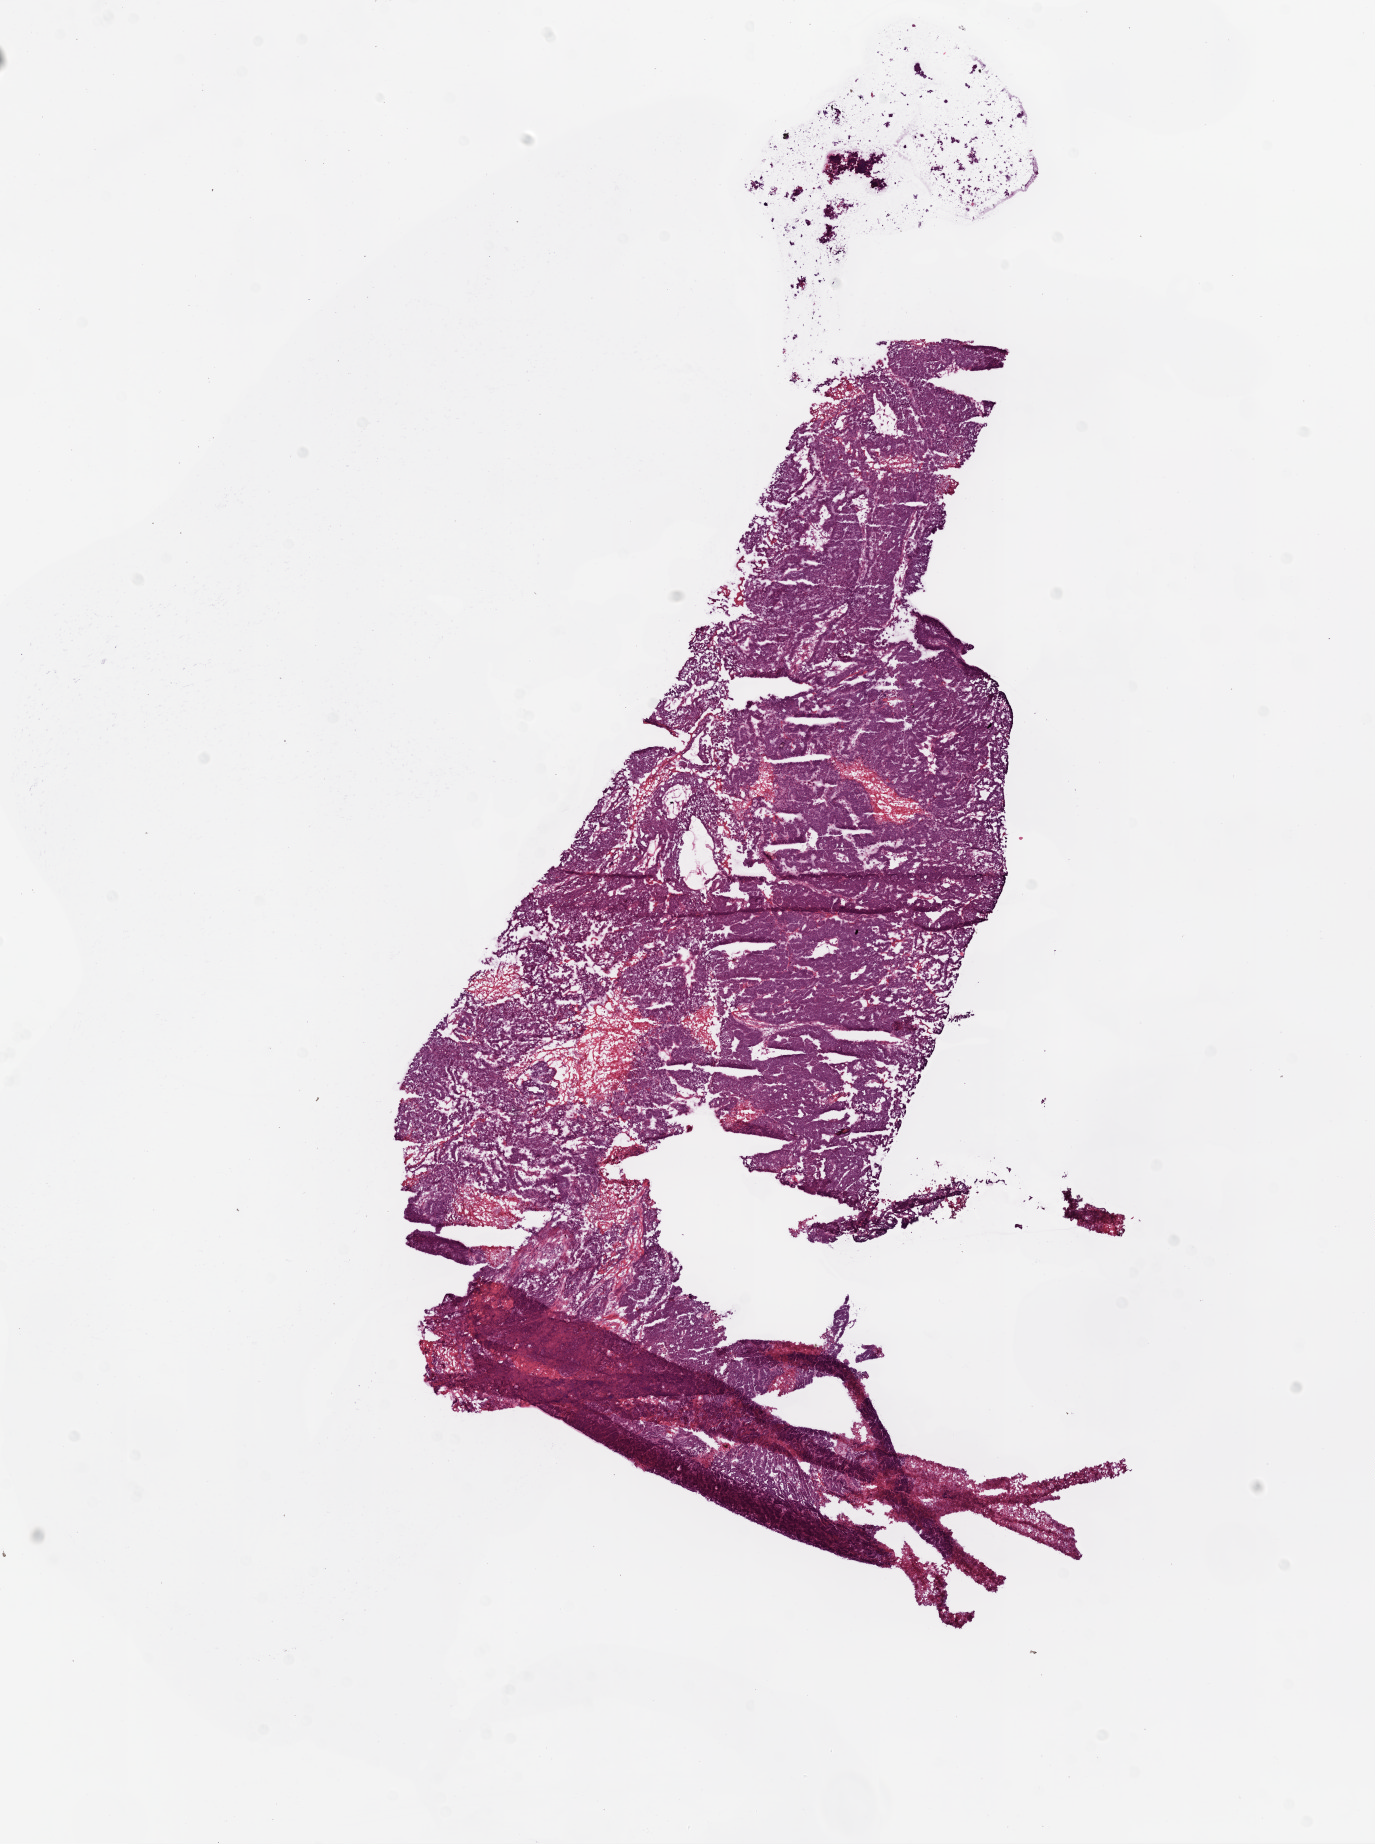
Hematoxylin and eosin (H&E) stained whole-slide image — shown as a low-resolution overview of the whole scanned area (about 11.0 x 14.8 mm, from a 20x scan), frozen section, sample: primary tumour, ovary. Female patient; age at initial diagnosis 42 years. Histologic grade: G3 (poorly differentiated). Pathologist review of this section (percent, as recorded): tumour cells 90%, tumour nuclei 90%, normal cells 0%, stromal cells 0%, necrosis 10%. Inflammatory infiltration, as recorded: lymphocyte infiltration 0%, monocyte infiltration 0%, neutrophil infiltration 10%.
- FIGO stage: IIIC
- diagnosis: Serous cystadenocarcinoma, NOS
- laterality: bilateral